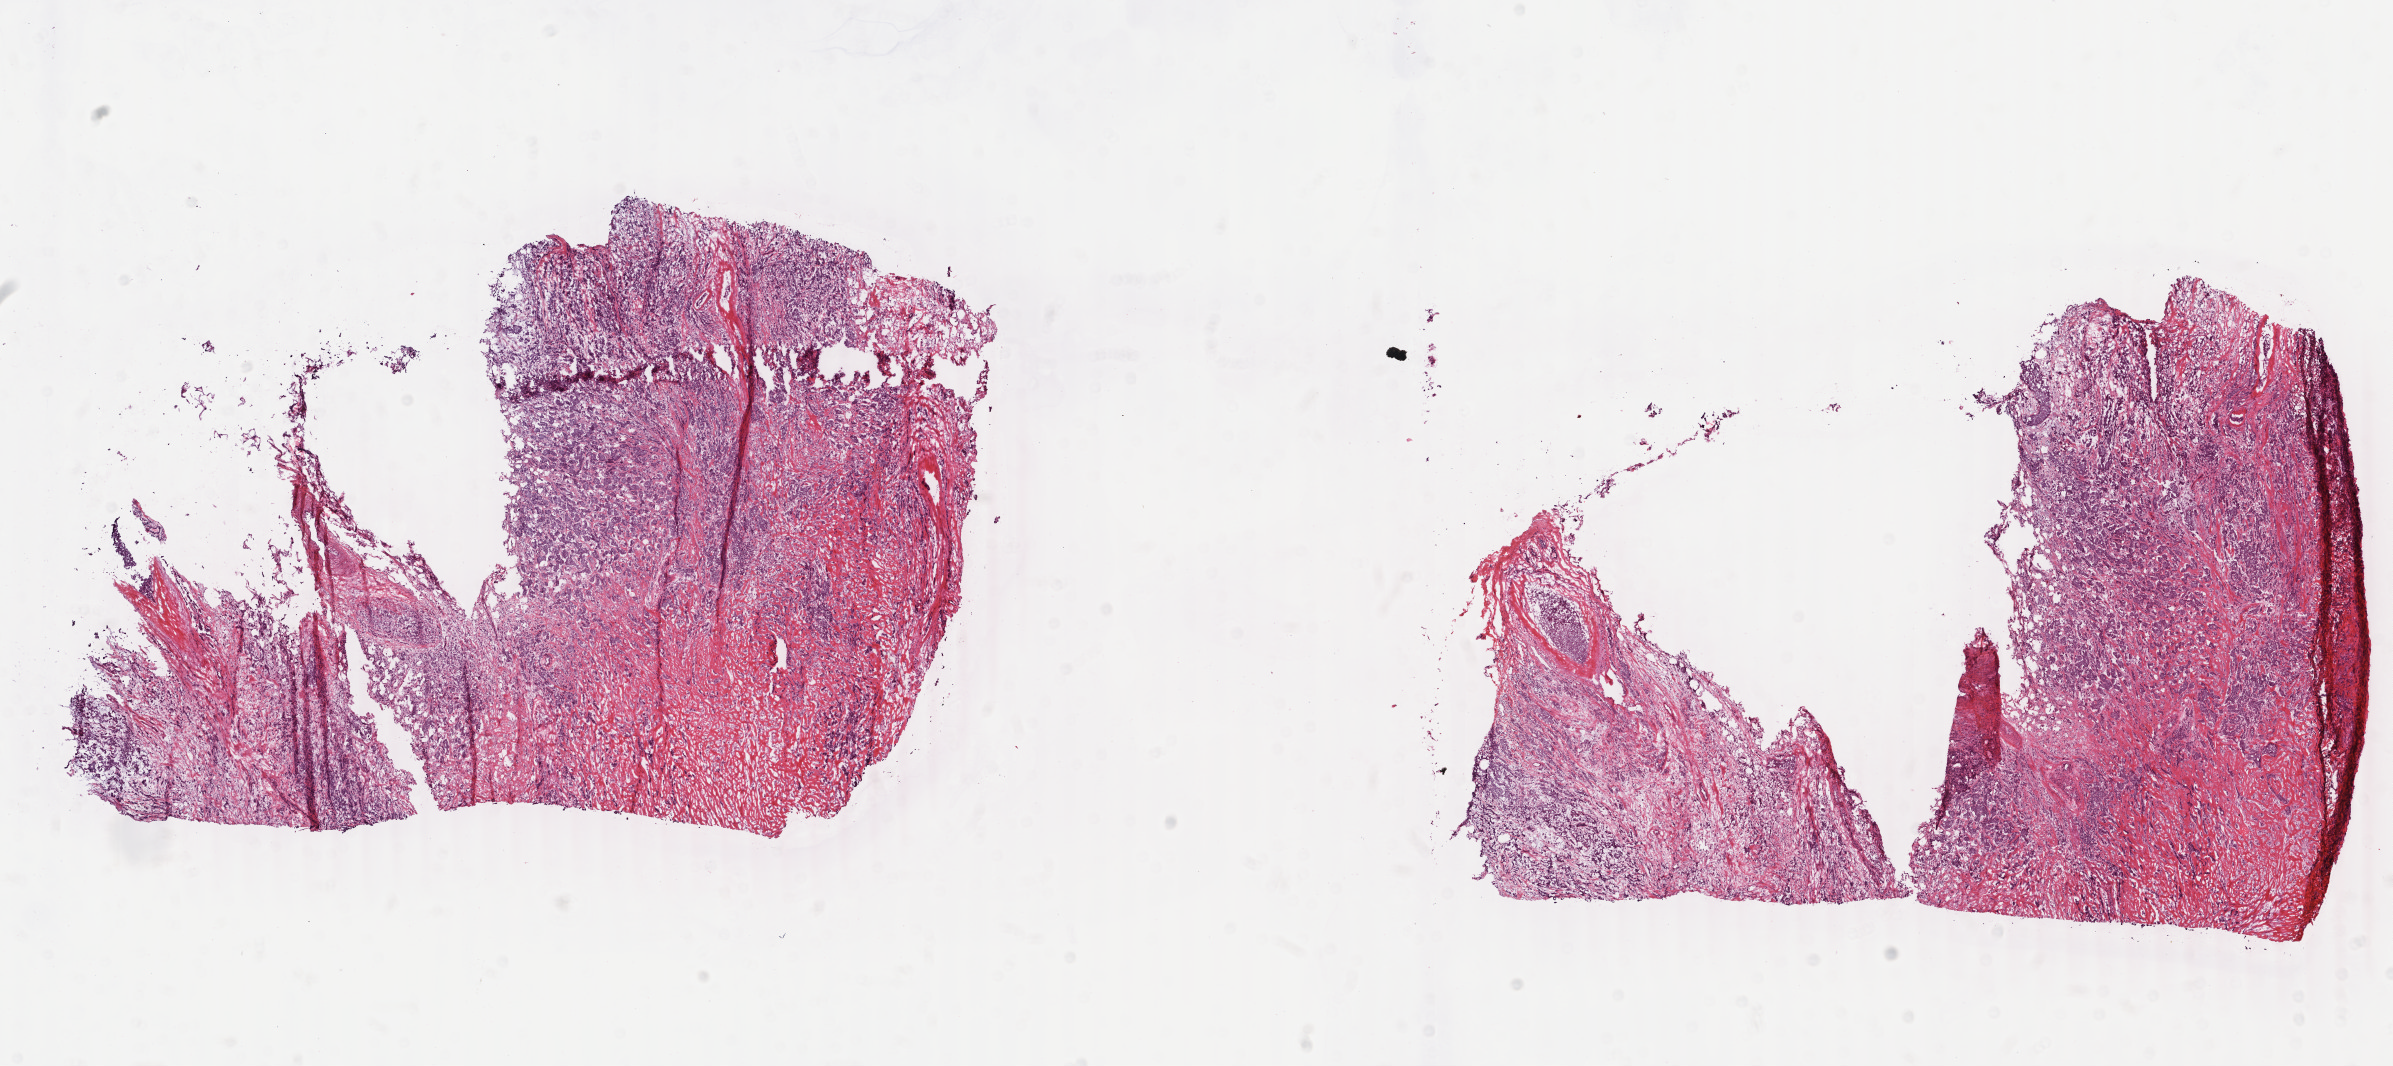
Digitized Hematoxylin and eosin (H&E) stained tissue section (whole slide), shown as a low-resolution overview of the whole scanned area (about 19.0 x 8.5 mm, acquisition: 40x scan), frozen section from the bottom of the tissue portion, primary tumour sample from the breast. Female patient; age at initial diagnosis 62 years. Slide review estimates, as recorded: tumour cells 60%, tumour nuclei 90%, normal cells 0%, stromal cells 38%, necrosis 2%. Inflammatory infiltration, as recorded: lymphocyte infiltration 1%, monocyte infiltration 0%, neutrophil infiltration 0%.
Diagnosis: Infiltrating duct carcinoma, NOS. Lymph nodes positive (case pathology): 0 of 9 examined. Laterality: left. AJCC pathologic stage: IIA.